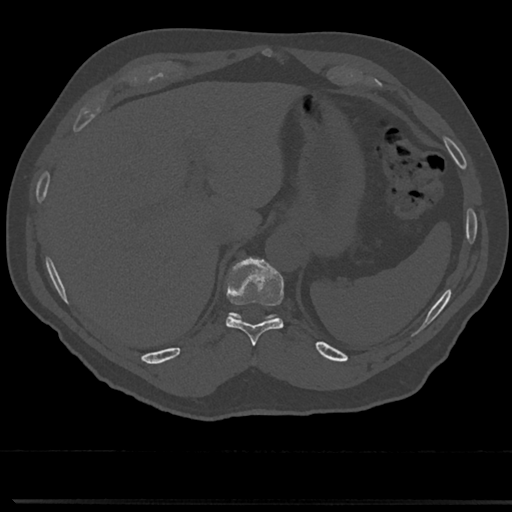
CT including the spine, one axial slice; slice 246 of 817 in the series (ordered by position); 120 kVp; bone window (W 1800 / L 400 HU); 0.5 mm slice thickness; 512 × 512 image matrix, field of view 355 × 355 mm. Patient: male, 61 years. From the clinical record (not read from this slice): primary cancer: prostate.
Annotated regions visible in this slice (semi-automatic segmentation, software-assisted and operator-edited):
- T10 vertebra: bounding box [x1, y1, x2, y2] px = [223, 257, 285, 344]
- T11 vertebra: [232, 314, 240, 319]
- T9 vertebra: [252, 355, 257, 361]